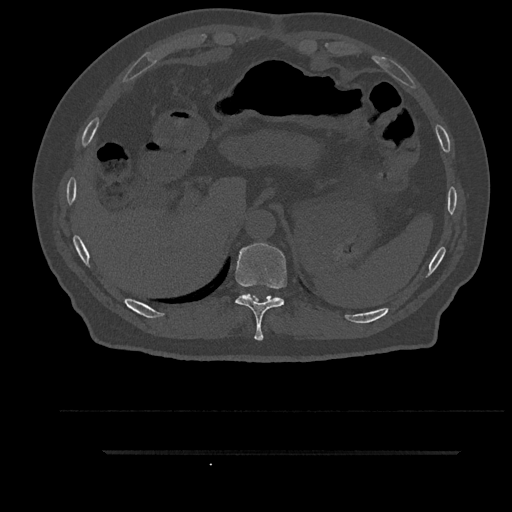
CT including the spine, one axial slice. Position 354 of 797 along the scan axis. 120 kVp. Bone window (W 1800 / L 400 HU). 0.5 mm slice thickness. 512 × 512 image matrix. Patient: male, 63 years. Case-level facts recorded for this patient, not image findings: primary cancer: renal; vertebrae with lytic lesions (as recorded): T8.
Annotated regions visible in this slice (semi-automatic segmentation, software-assisted and operator-edited):
- T10 vertebra: bounding box (x1, y1, x2, y2) in pixels: (235, 243, 287, 341)
- T11 vertebra: (244, 294, 279, 299)